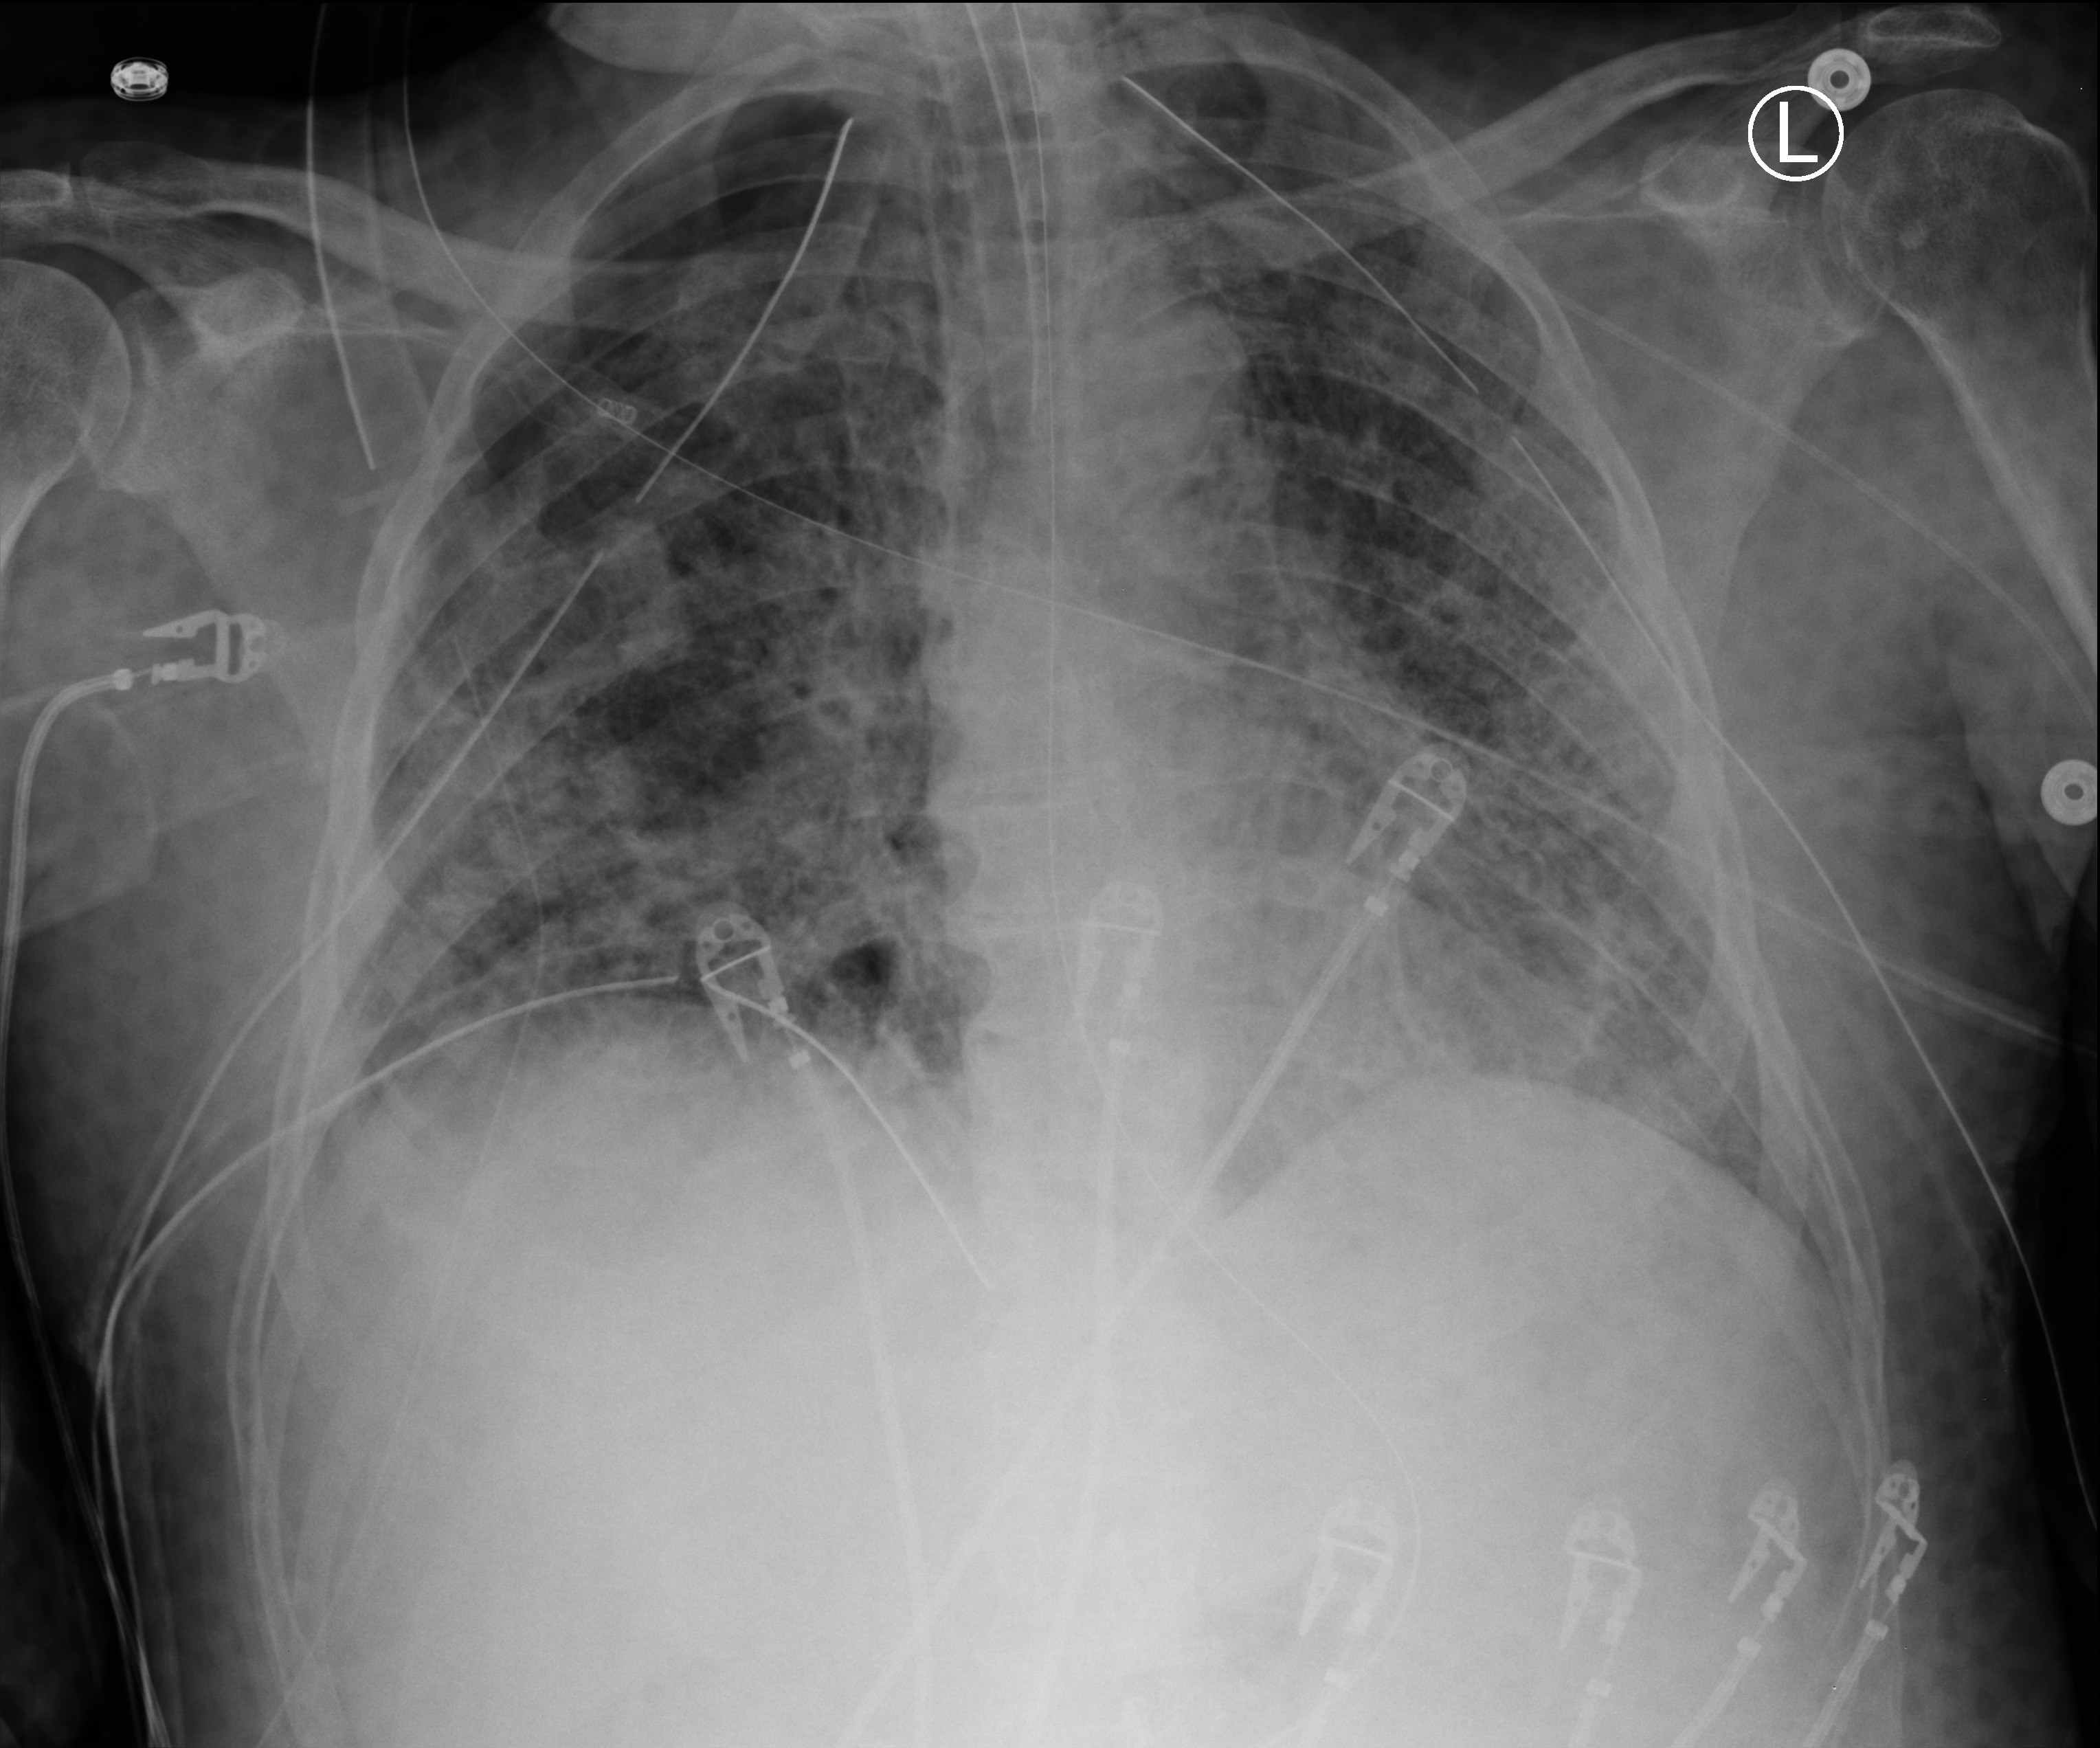
Portable chest radiograph, anteroposterior (AP) projection. Patient hospitalised with COVID-19; male, aged 18–59 years.
From the hospital-stay record, not from the radiograph (when in the stay this image was taken is not recorded): mechanically ventilated during this hospital stay: yes; smoking status (admission record): never; length of hospital stay: 83 days.